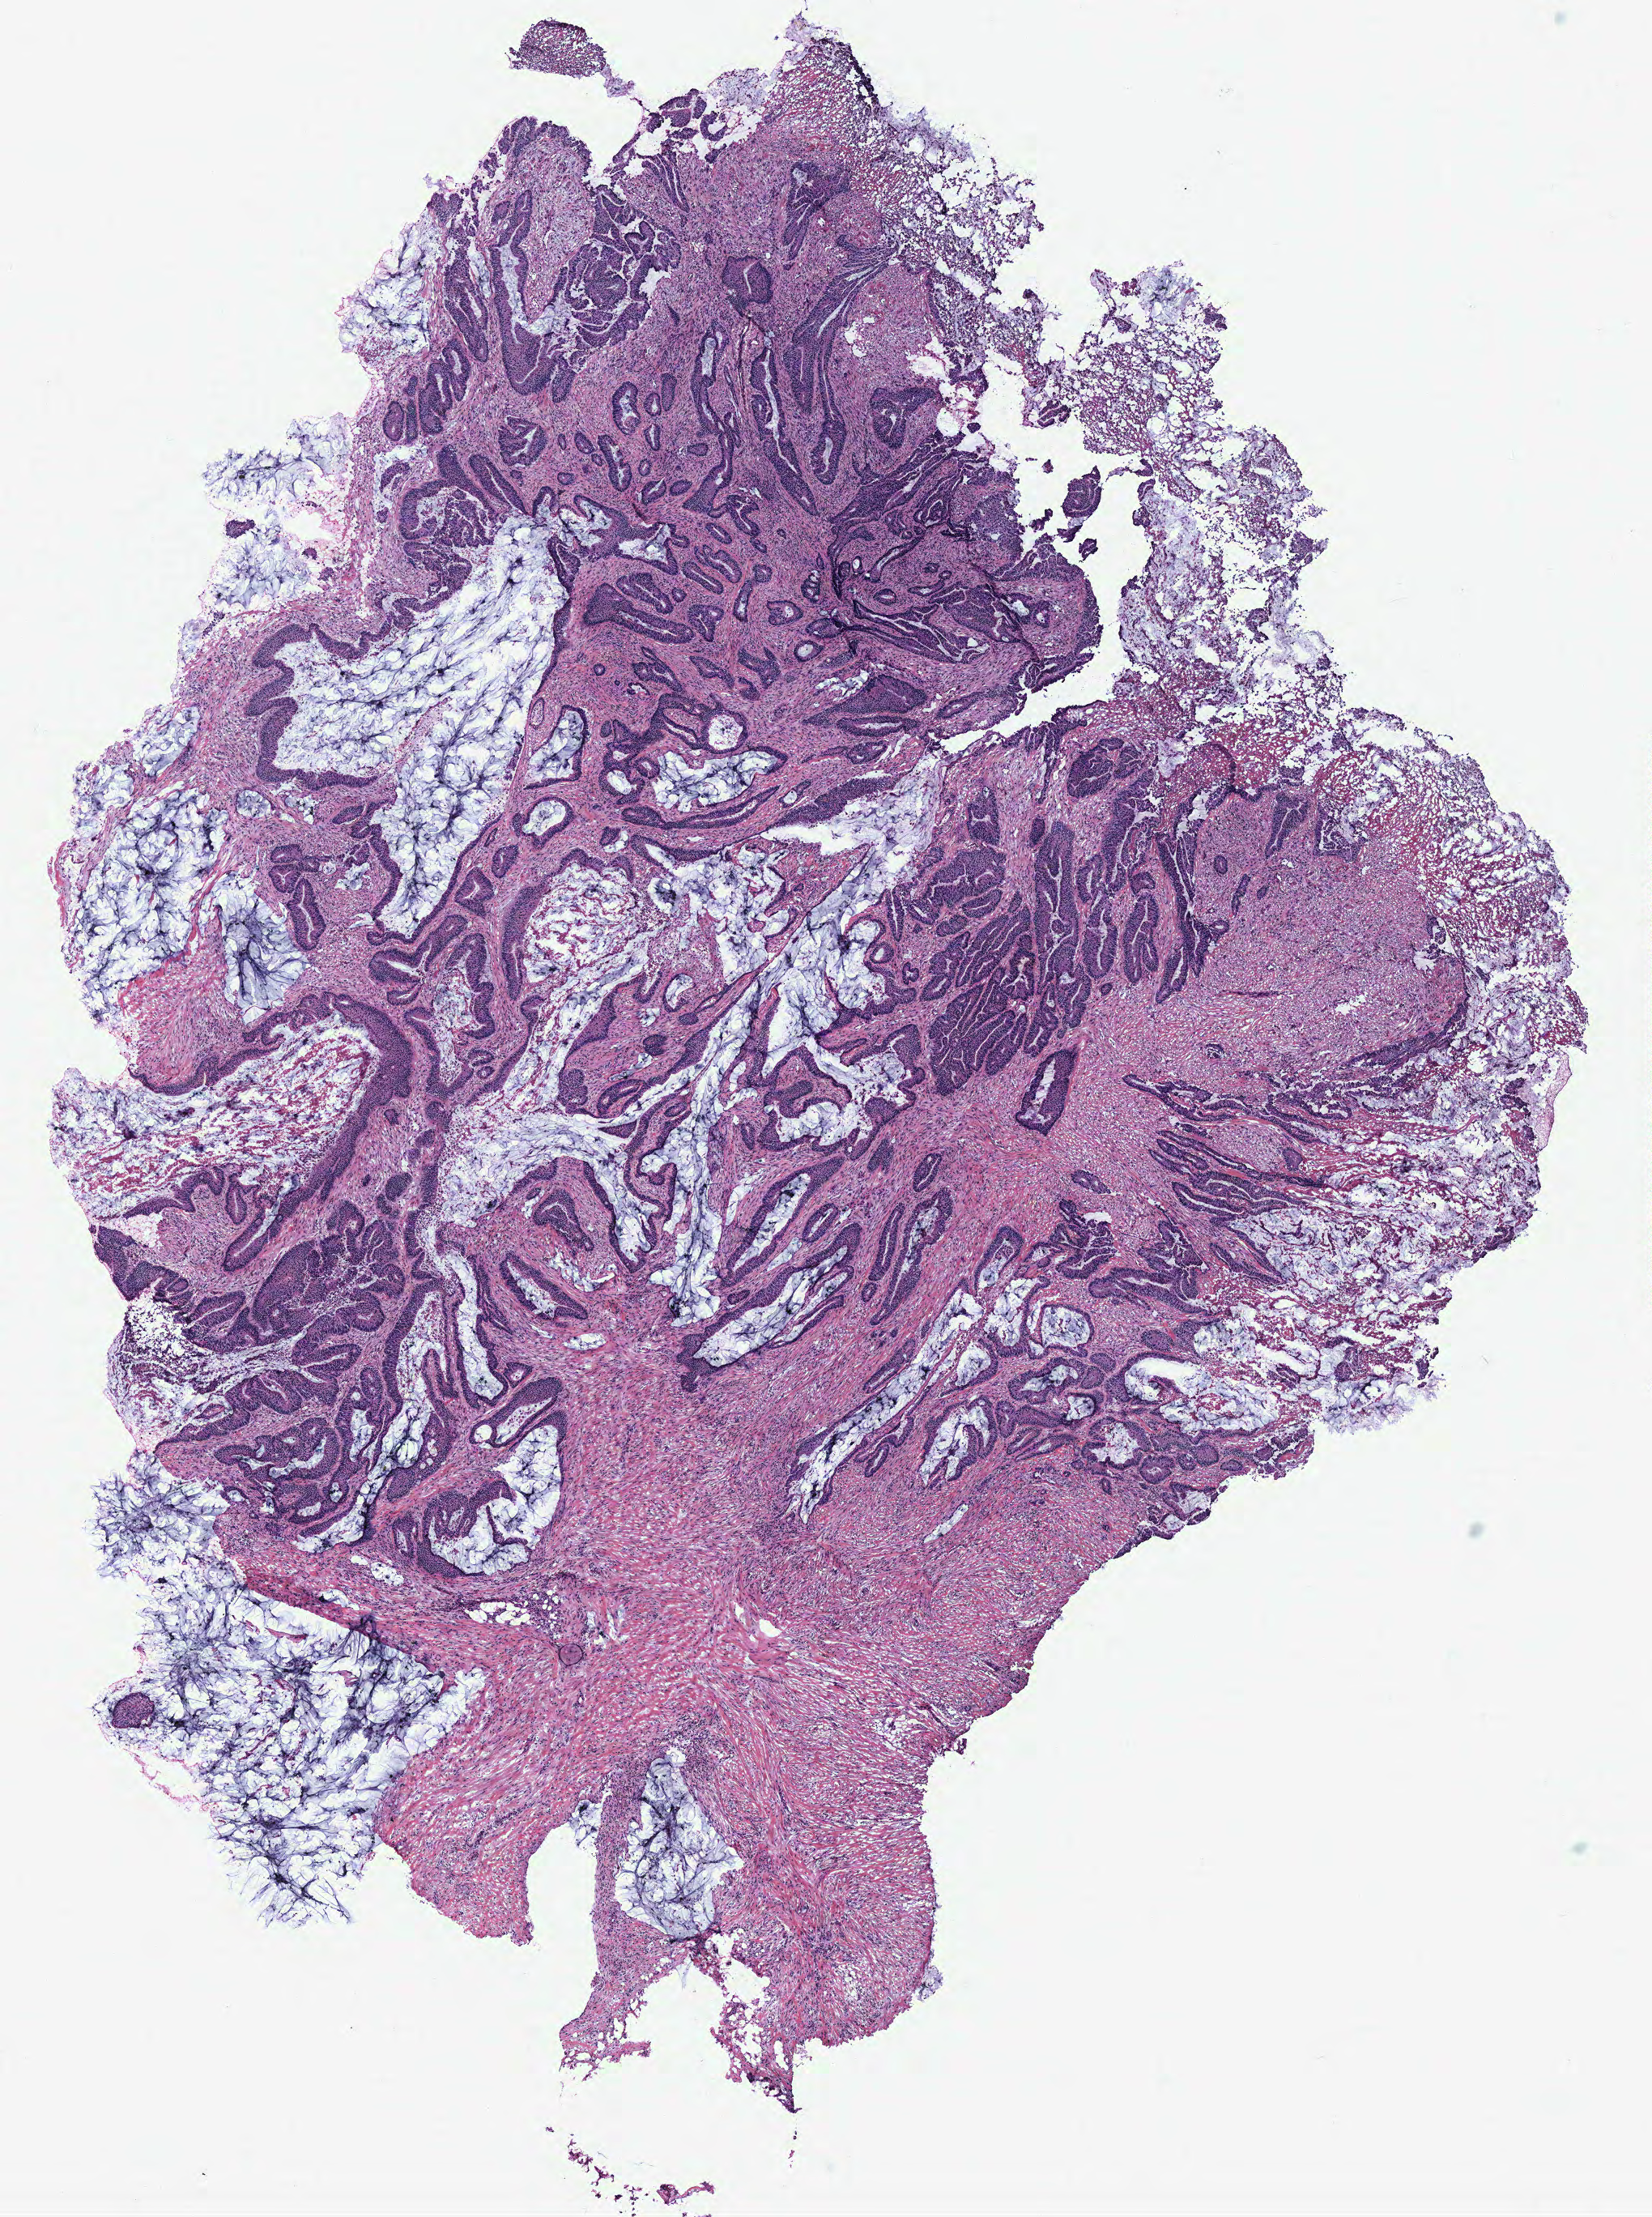
Digitized Hematoxylin and eosin (H&E) stained tissue section (whole slide), shown as a low-resolution overview of the whole scanned area (about 8.2 x 11.0 mm). Tumour tissue sample, colon. Patient: male, age 50 years.
AJCC pathologic stage: IIA. Diagnosis: Adenocarcinoma, NOS. Primary tumour site (as recorded): colon.